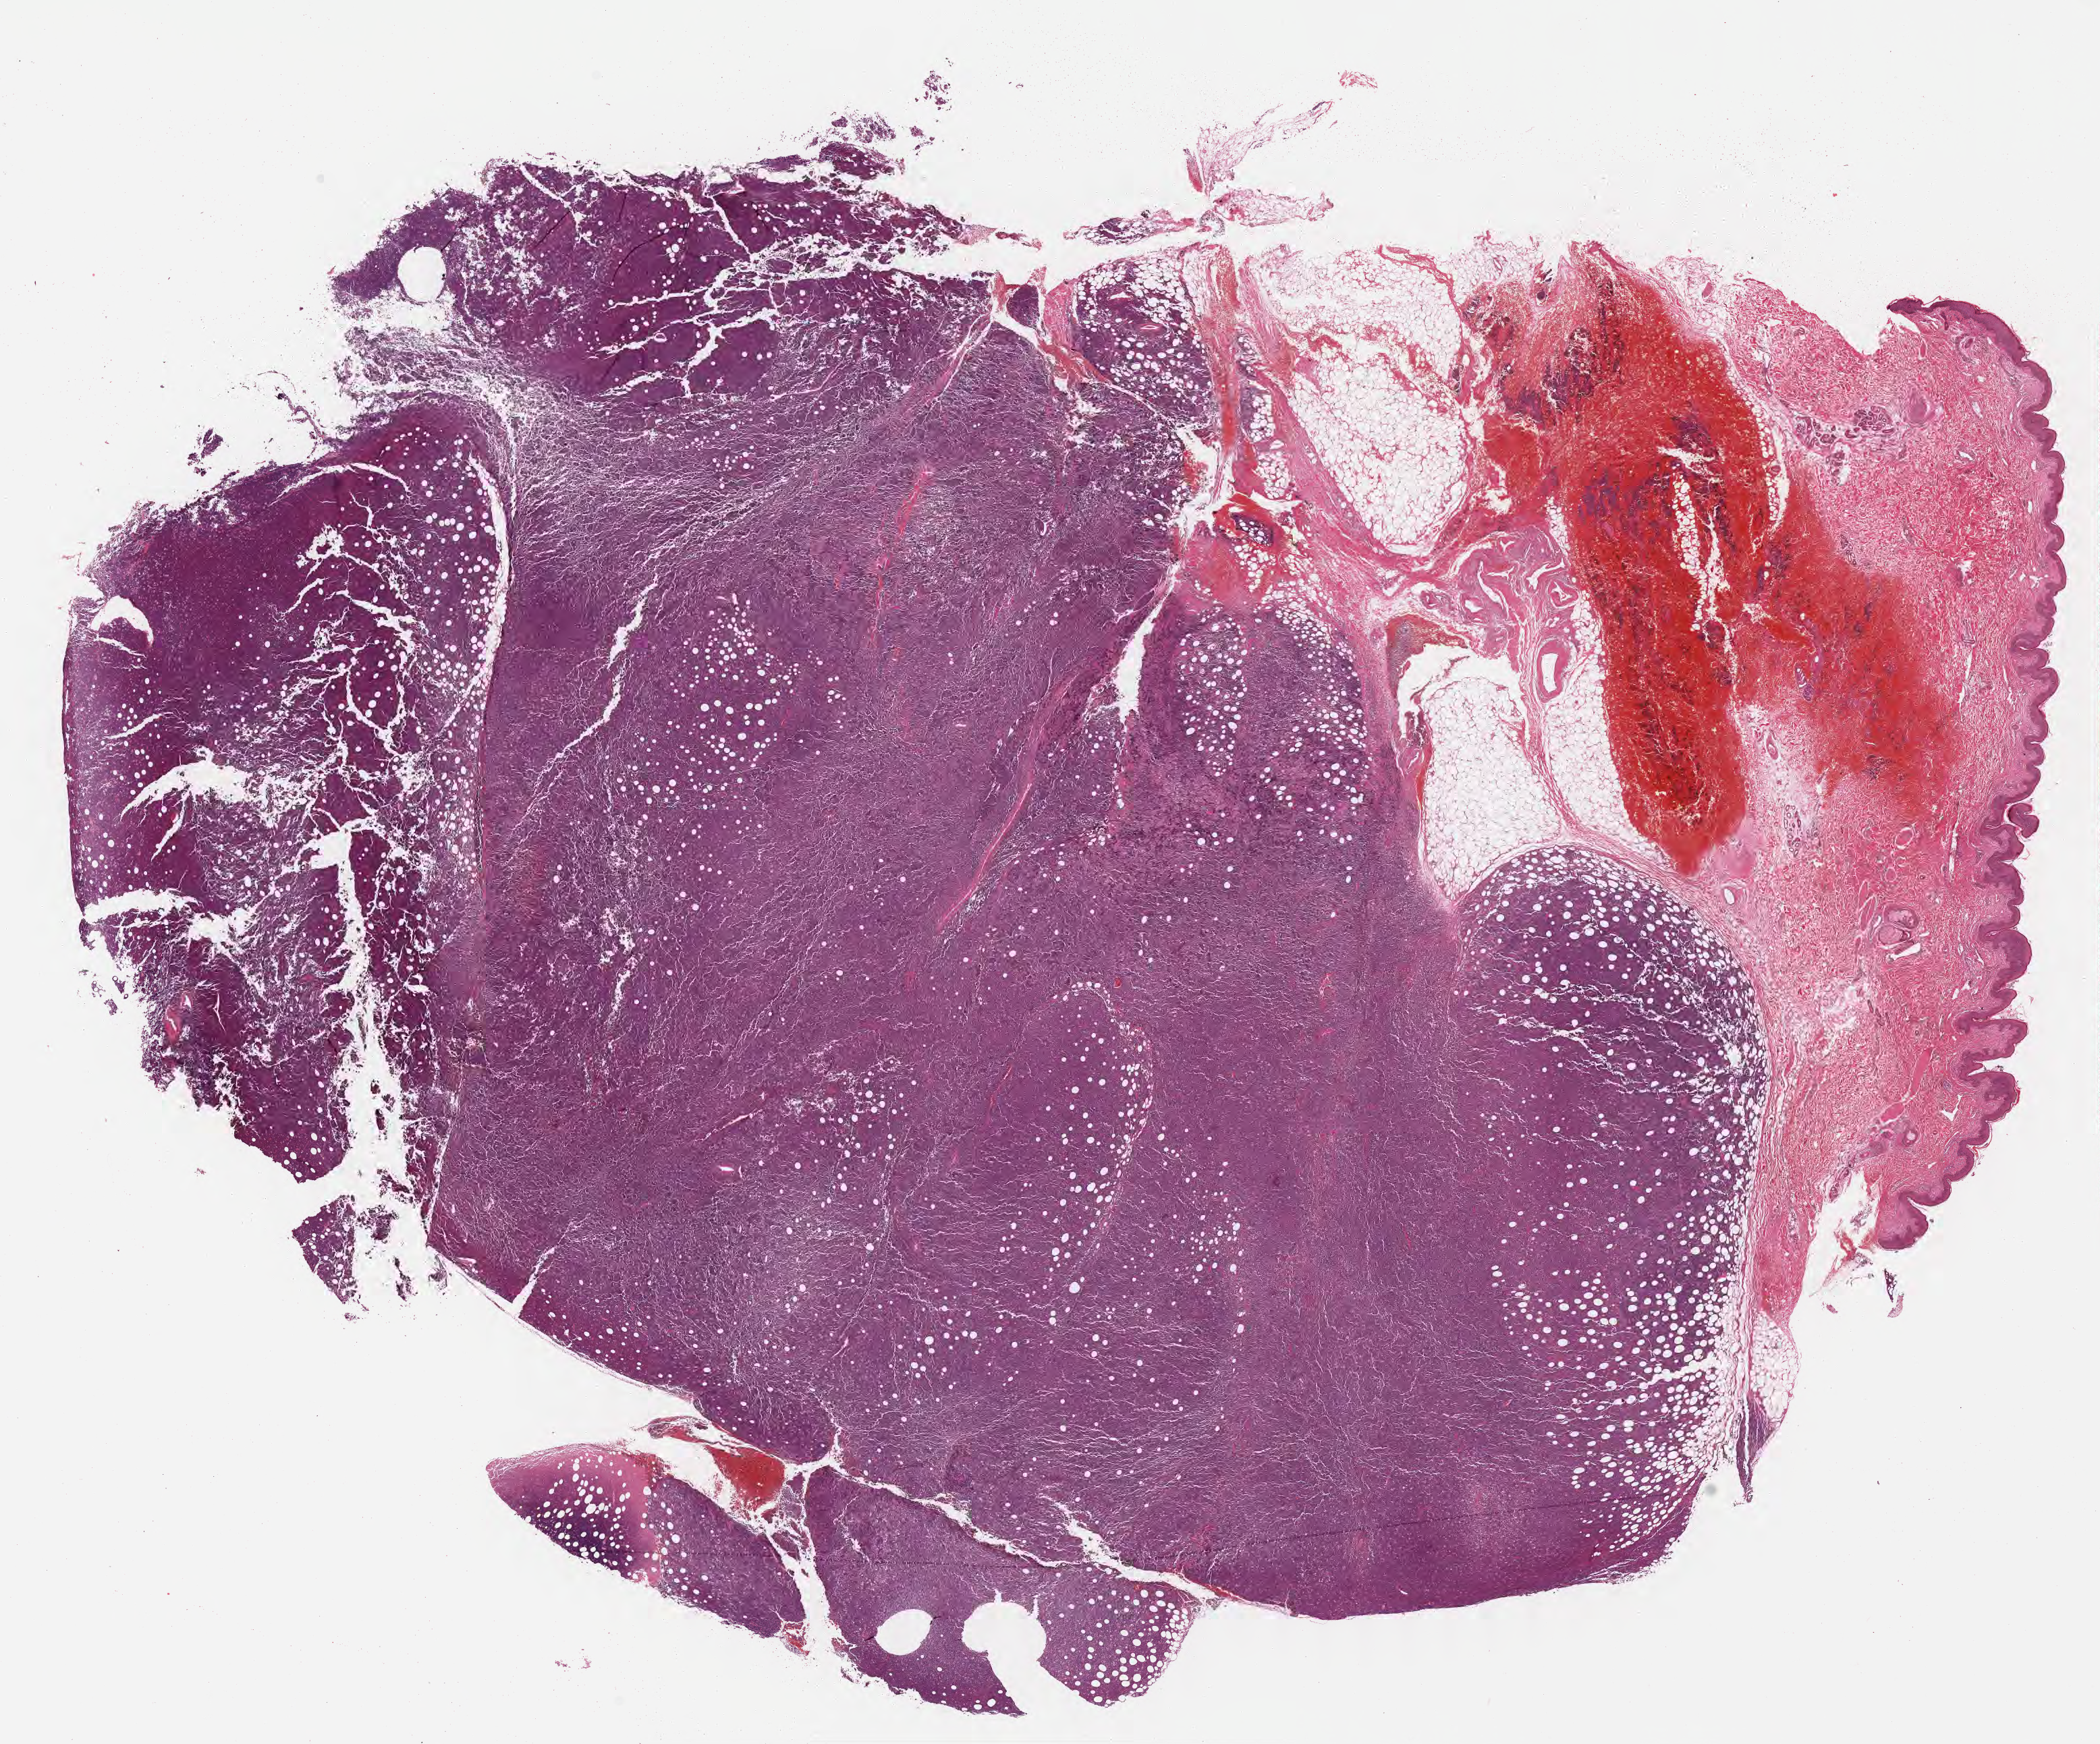
Haematoxylin and eosin whole-slide image, whole scanned area (about 25.1 x 20.9 mm) shown as a low-resolution overview, formalin-fixed, paraffin-embedded (FFPE) tissue, primary tumor. Male patient, 52 years old. Slide review estimates, as recorded: tumor cells 70%, tumor nuclei 95%, stromal cells 0%, necrosis 5%, normal cells 25%. Infiltration values recorded for this section: lymphocyte infiltration 70%, monocyte infiltration 15%, neutrophil infiltration 0%.
• Ann Arbor stage (patient): Stage IV
• section: bottom of the tissue portion
• histologic diagnosis: Burkitt lymphoma, NOS